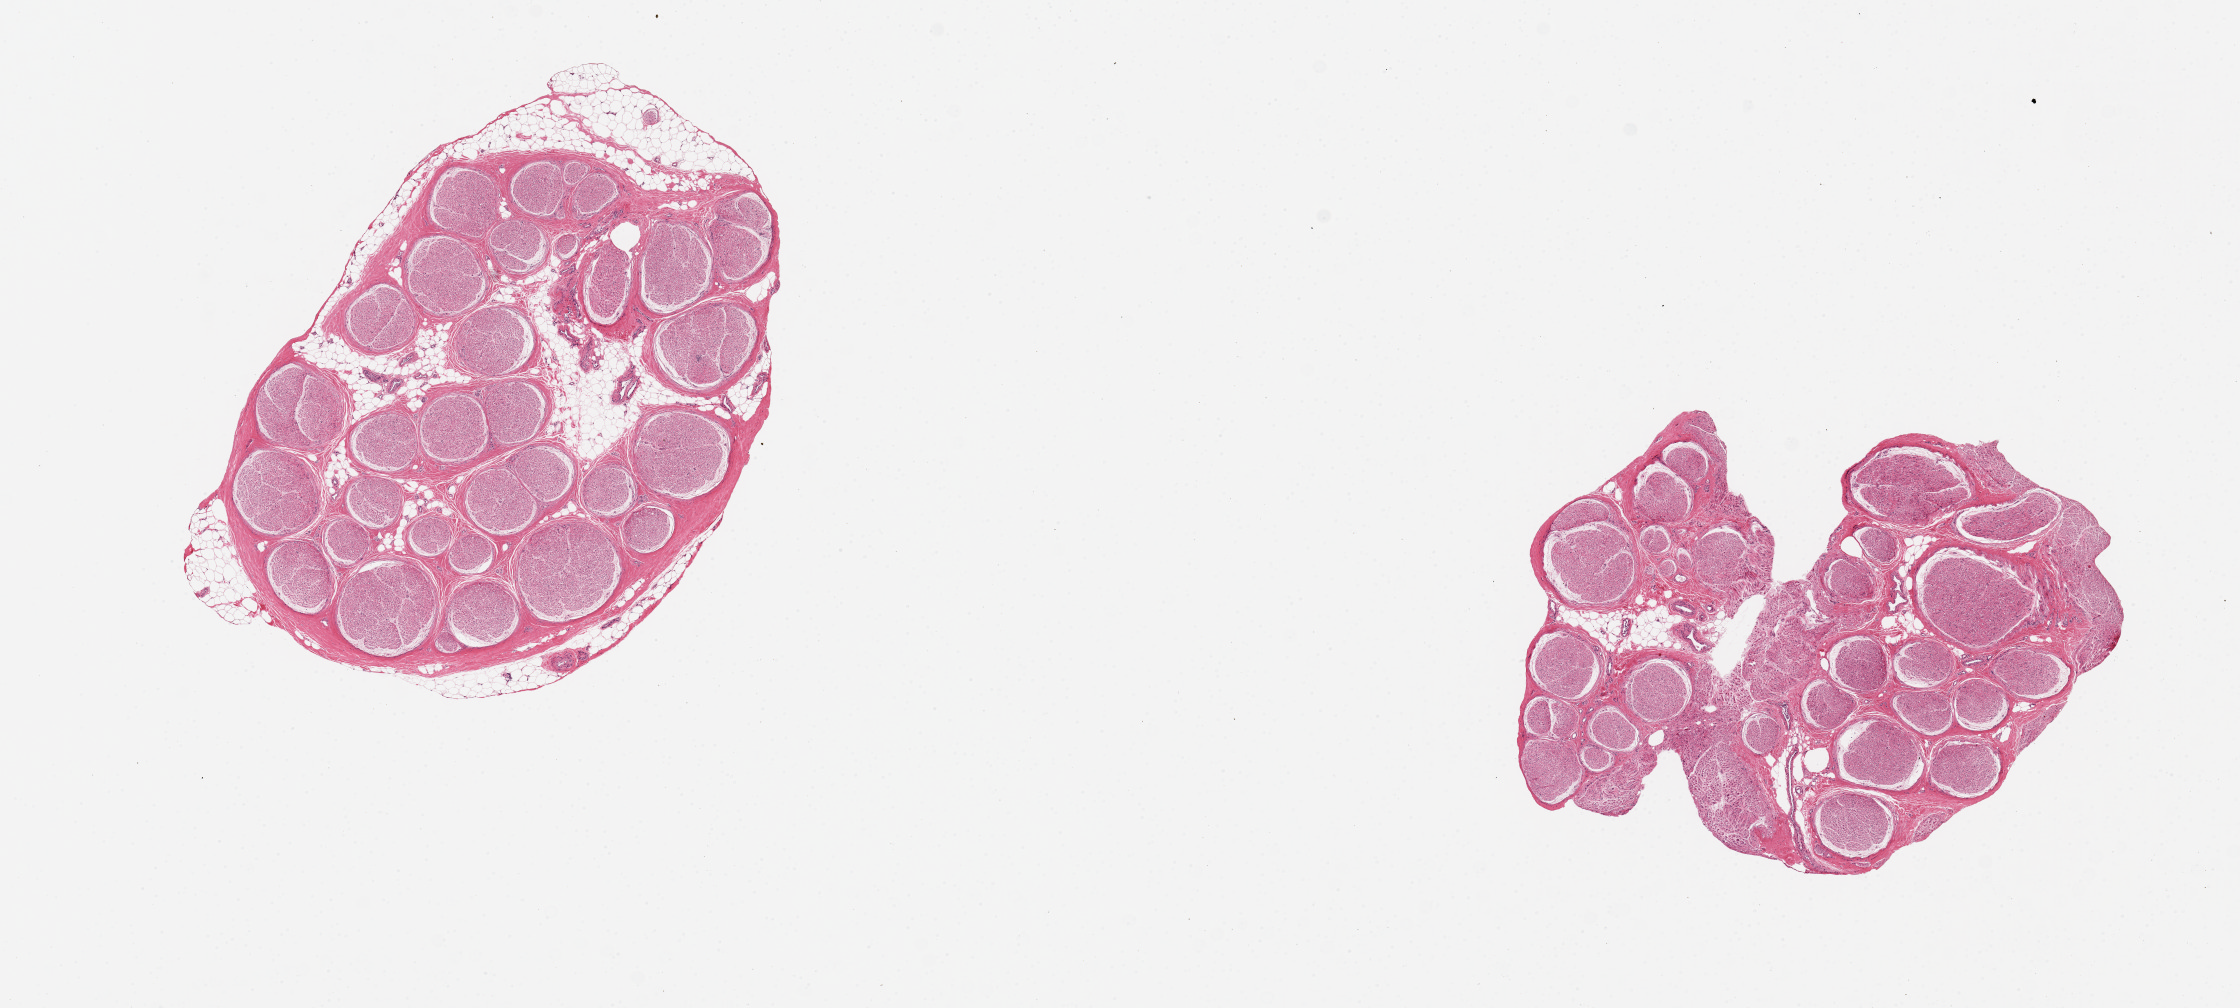
Haematoxylin and eosin whole-slide image — low-resolution overview of the scanned area, about 17.7 x 8.0 mm; PAXgene-fixed, paraffin-embedded tissue; section of tibial nerve (target tissue); donor tissue sample.
Pathologist's review note for this sample: 2 pieces; rim of discontinuous fat on one, up to ~0.5mm; fairly clean specimens.